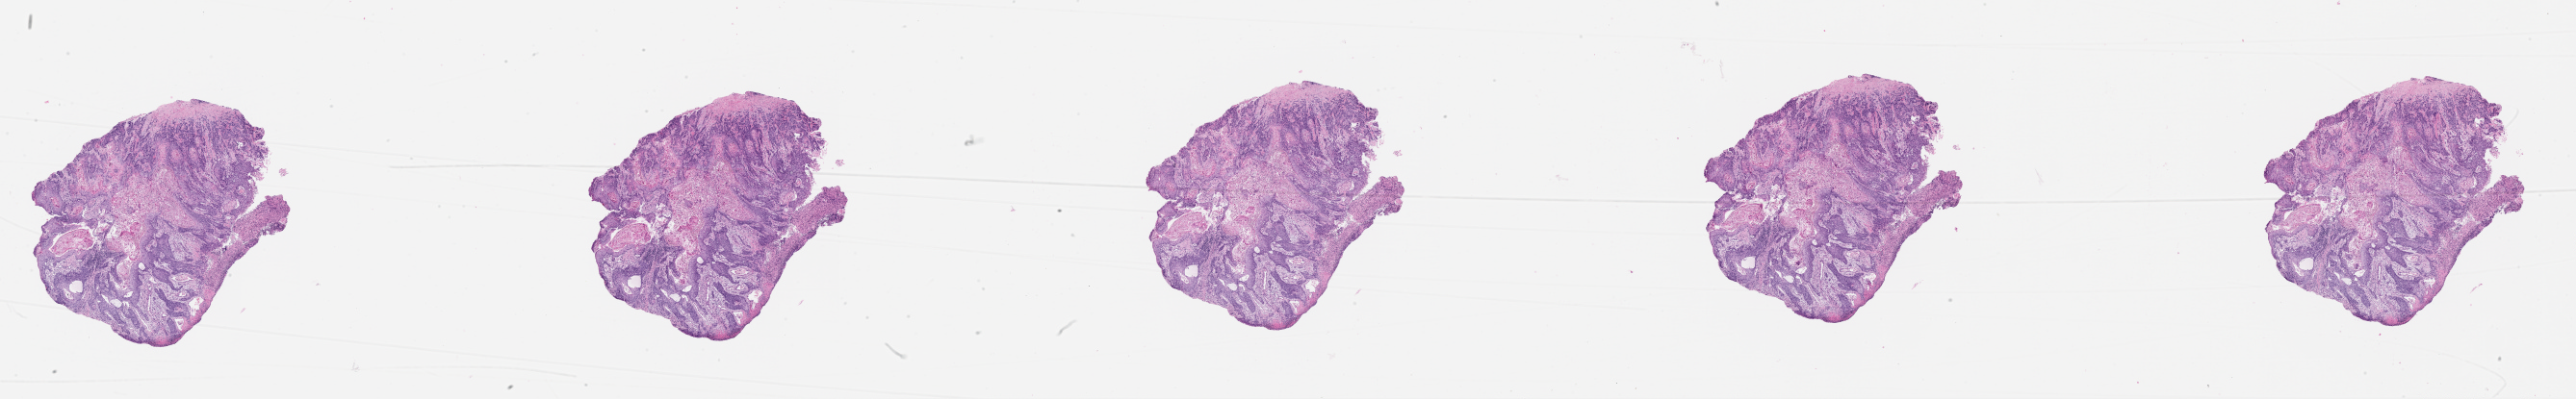
Whole-slide histology image, H&E — whole scanned area (about 43.1 x 6.7 mm, acquisition: 20x scan) shown as a low-resolution overview. Head and neck, tissue type not recorded. Female, 60 y/o.
Patient diagnosis: Squamous cell carcinoma, NOS (tonsil, NOS).